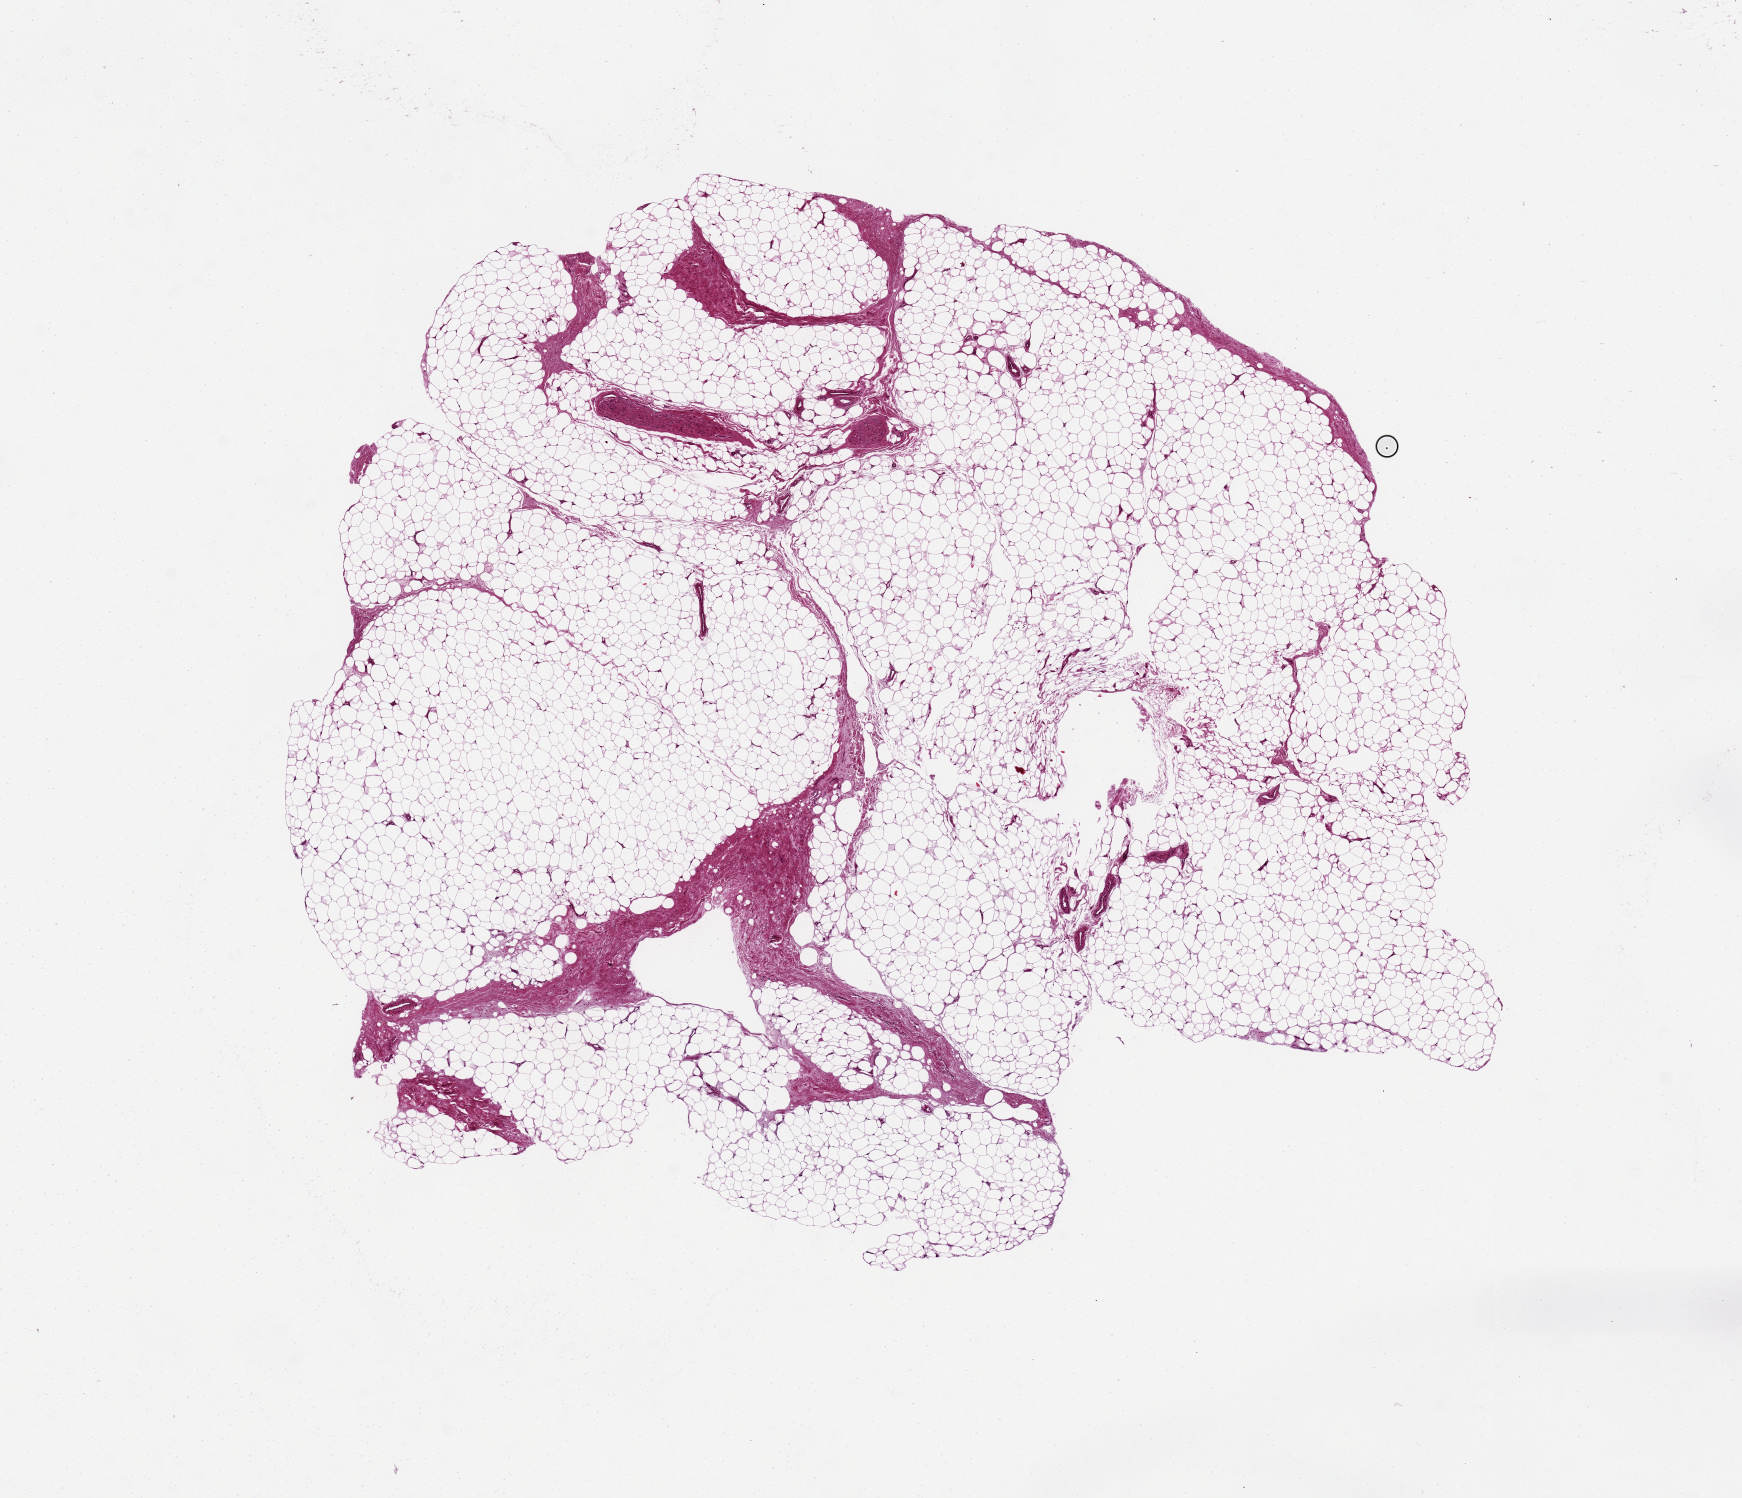
Whole-slide image, haematoxylin and eosin stain, brightfield, a low-resolution overview of the entire scanned area, about 13.8 x 11.9 mm (from a 20x scan), PAXgene-fixed, paraffin-embedded tissue, sampled site (target tissue): adipose tissue, tissue donor sample. Male donor.
Pathologist's review note for this sample: 7x9 mm. well fixed tissue.